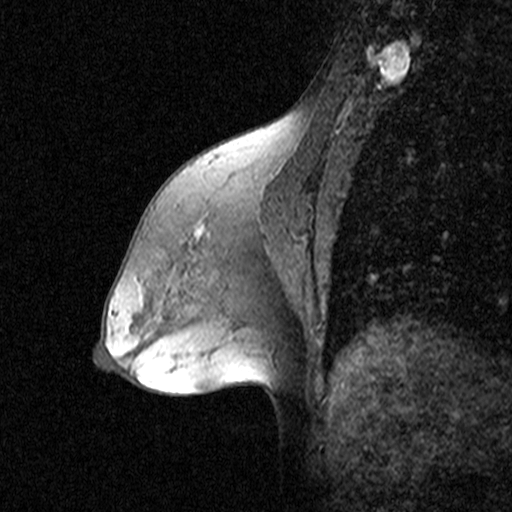
Breast MRI (dynamic contrast-enhanced), one sagittal slice; slice 24 of 44 in the series (ordered by position); dynamic contrast-enhanced study with each time point stored as its own series, time point 2 of 3 at this slice position (early post-contrast, ordered by acquisition time); 1.5 T; TE 4.5 ms, TR 11 ms; 3 mm slice thickness; 512 × 512 image matrix, field of view 200 × 200 mm. Female patient, age 53 years. From the clinical record (not read from this slice): setting: breast cancer imaged before/during neoadjuvant chemotherapy; receptor status: HR-positive, HER2-negative.
Outlined on this slice (semi-automatically segmented with operator editing):
- analysis volume of interest (the breast-tissue region the enhancement analysis was run in; not a lesion): bounding box <176,178,299,305> (left, top, right, bottom; pixels)
- tumour enhancement mask (voxels above the 90 % enhancement threshold inside the analysis volume of interest): <198,230,201,236>